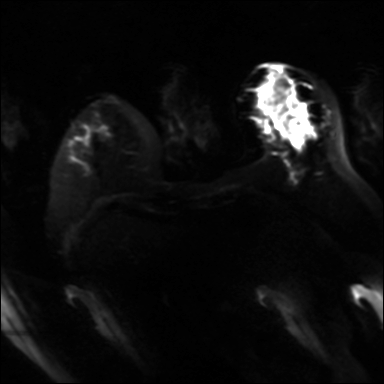
Breast MRI, one axial slice; slice 11 of 36 in the series (ordered by position); diffusion-weighted series; image 2 of 4 stored at this slice position (different b-values; order by instance number); 3 T; 4 mm slice thickness; 384 × 384 image matrix. Female patient.
Structures marked on this image (outlined manually by an expert reader):
- tumour on diffusion-weighted imaging: box from (x=288, y=115) to (x=310, y=138) px